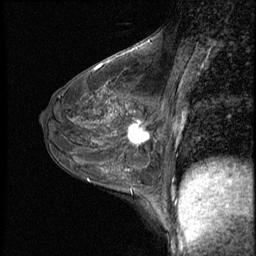
Breast MRI (dynamic contrast-enhanced), one sagittal slice. Position 31 of 50 along the scan axis. 3 images stored at this slice position (order not interpretable as contrast timing). 1.5 T. TE 4.2 ms, TR 8.7 ms. 256 × 256 image matrix, field of view 180 × 180 mm. Female patient, age 43 years. Case-level facts recorded for this patient, not image findings: setting: breast cancer imaged before/during neoadjuvant chemotherapy; receptor status: HR-positive, HER2-negative.
Outlined on this slice (semi-automatic segmentation, software-assisted and operator-edited):
- analysis volume of interest (the breast-tissue region the enhancement analysis was run in; not a lesion): bounding box <122,109,159,155> (left, top, right, bottom; pixels)
- tumour enhancement mask (voxels above the 140 % enhancement threshold inside the analysis volume of interest): <128,123,150,146>